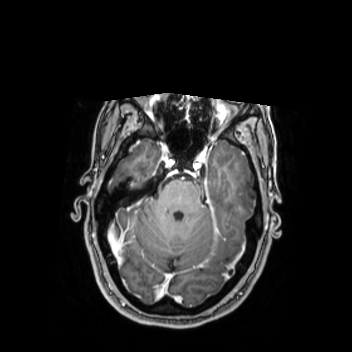
Brain MRI from a brain-tumour surgery series, one axial slice. Position 175 of 350 along the scan axis. T1-weighted post-contrast. 0.9 mm slice thickness. 352 × 352 image matrix. Case-level facts recorded for this patient, not image findings: histopathology: Oligodendroglioma; WHO grade: 2; IDH mutation: yes; tumour location: Left Middle Temporal Gyrus.
Outlined on this slice (manually delineated by an expert):
- tumour: bounding box (x1, y1, x2, y2) in pixels: (224, 170, 262, 200)